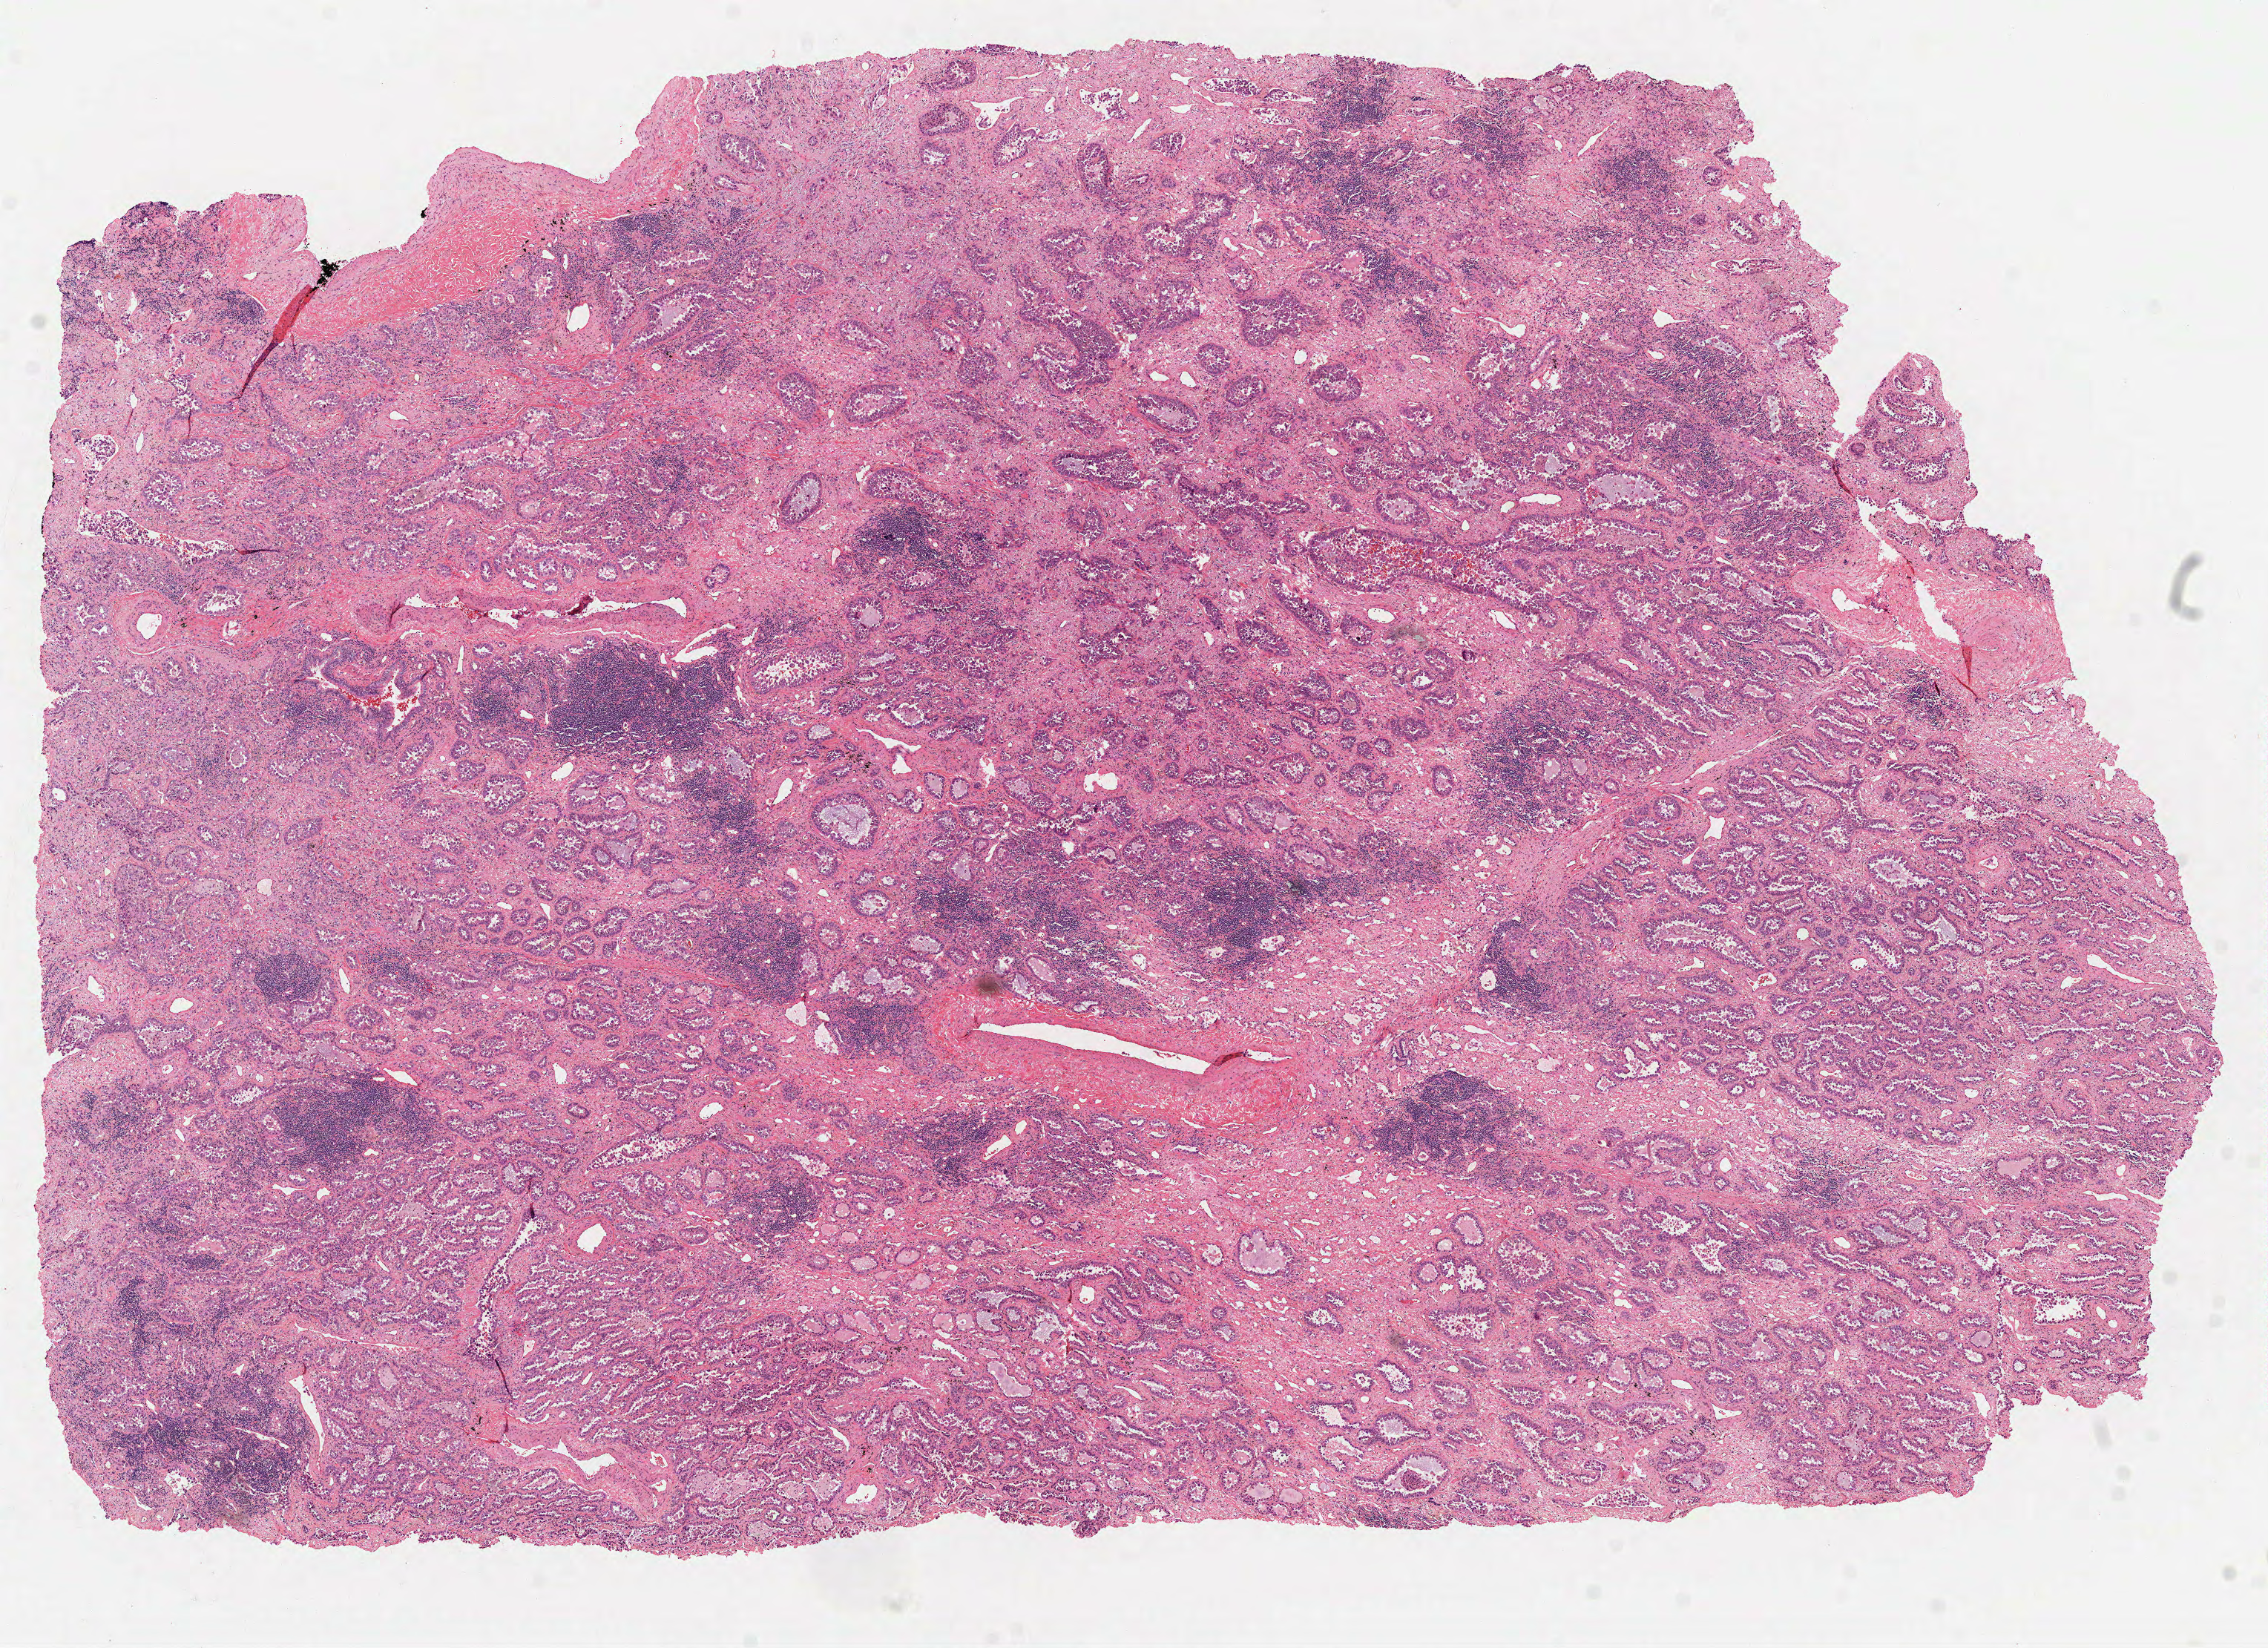
Whole-slide histology image, H&E, low-resolution overview of the scanned area, about 12.3 x 9.0 mm (acquisition: 40x scan). Formalin-fixed paraffin-embedded (FFPE) diagnostic section. Primary tumour sample from the lung. Female, age 58 years at initial diagnosis.
• pathologic diagnosis: Adenocarcinoma, NOS (upper lobe, lung)
• AJCC pathologic stage: IB (7th edition)